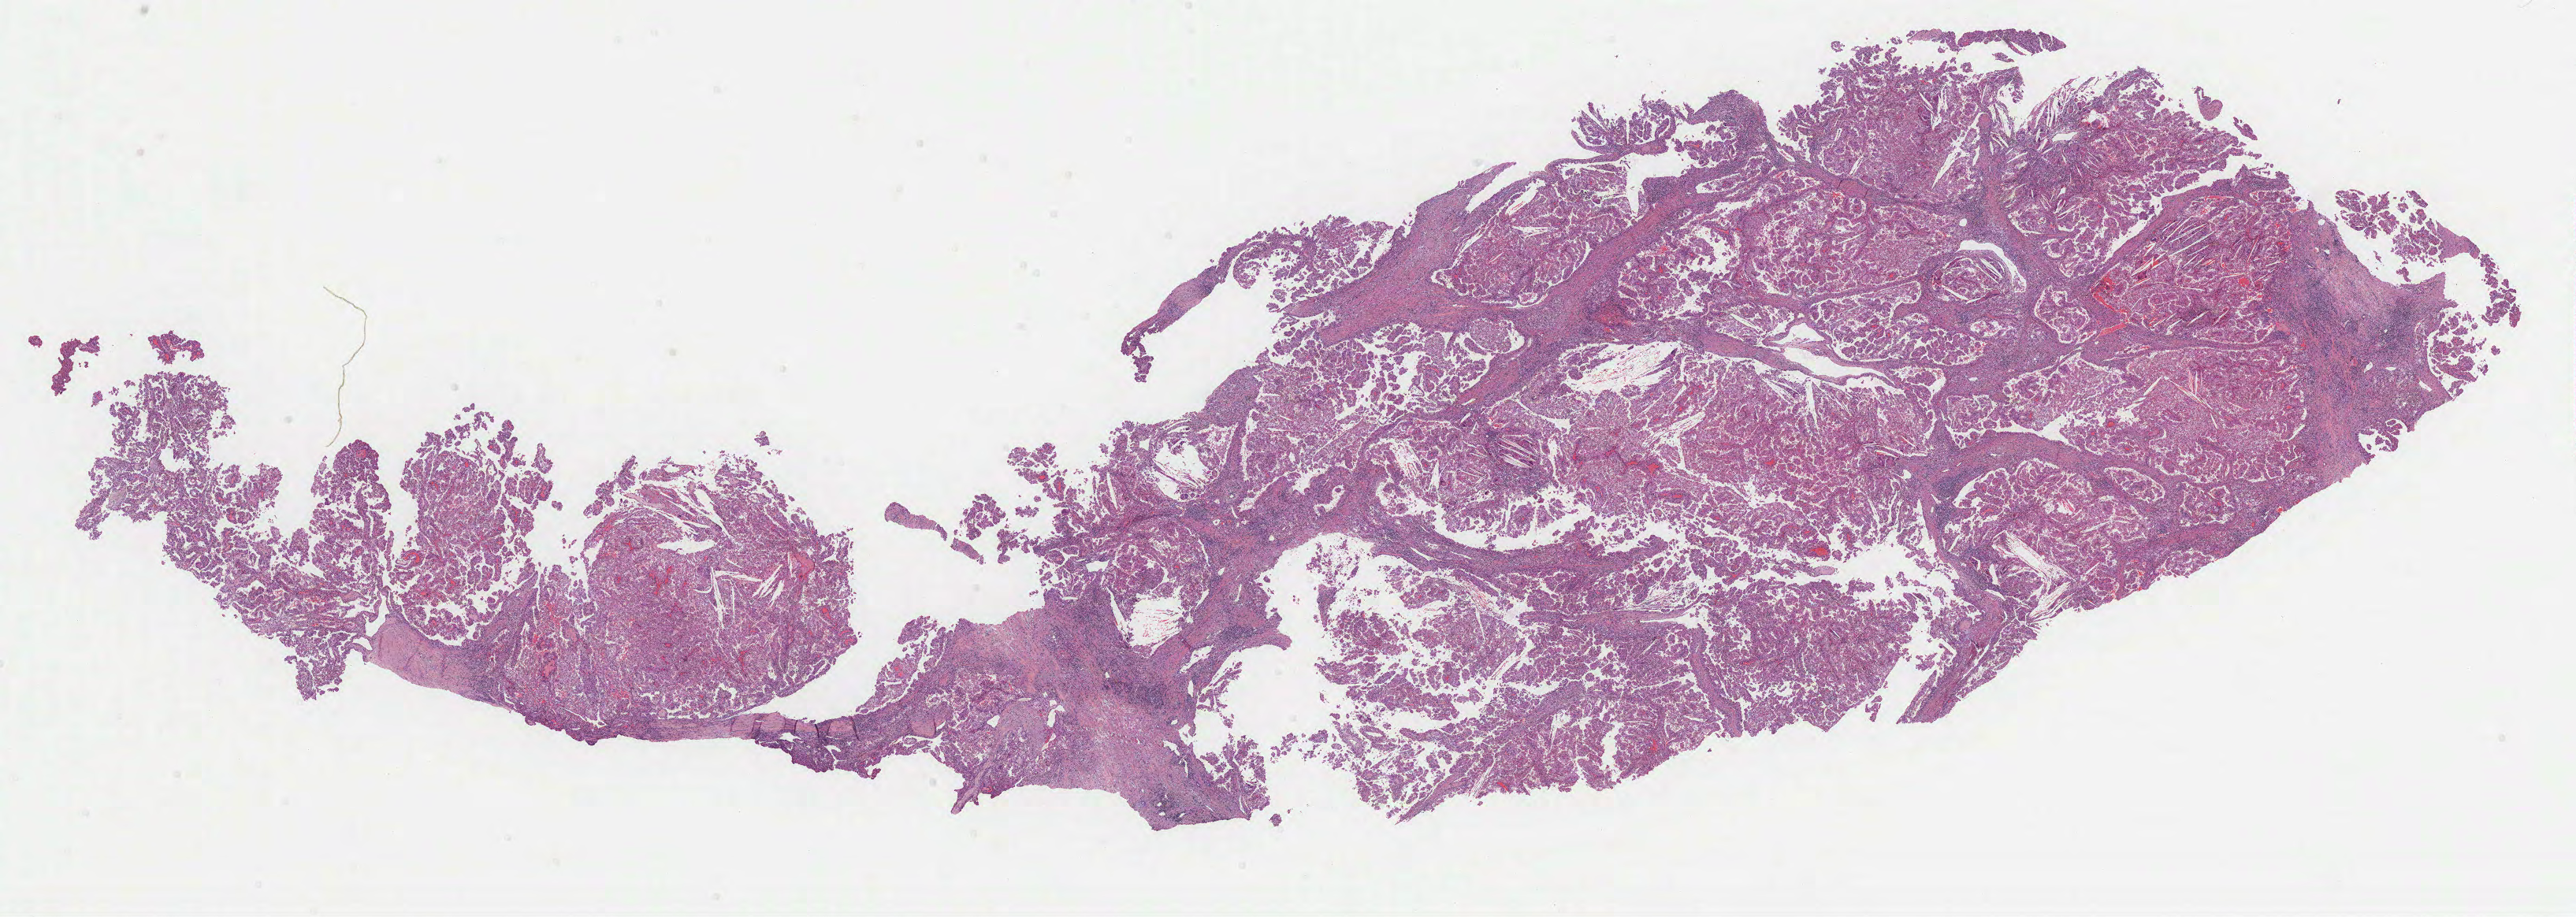
Whole-slide histology image, Hematoxylin and eosin (H&E) stained — whole scanned area (about 26.4 x 9.4 mm) shown as a low-resolution overview. FFPE section. Sample: primary tumour, kidney. Male, age 50 years at initial diagnosis.
Diagnosis: Papillary adenocarcinoma, NOS. AJCC pathologic stage: III.